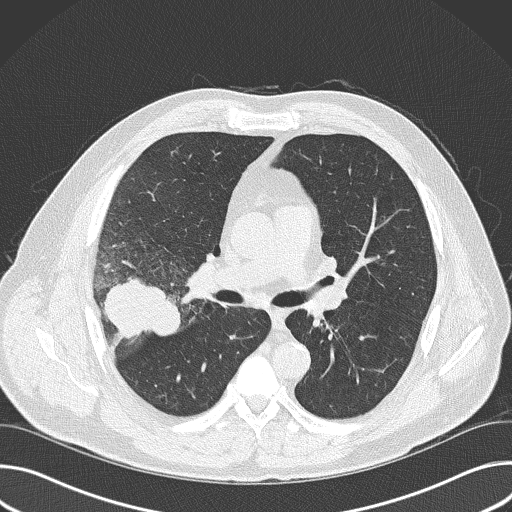
Low-dose screening chest CT, axial slice, first (baseline) screen, lung window (W 1500 / L -600 HU), lung (sharp) reconstruction kernel (B50f), slice 97 of 157 in the series. Male participant, aged 56 years at enrolment.
Lesion marked by an expert reader, box from (x=80, y=258) to (x=184, y=362) px. The exam's reader record, not a measurement of the box and not confirmed to be the same lesion: non-calcified nodule or mass ≥4 mm, right upper lobe, 6 × 5 mm, spiculated (stellate) margins, soft tissue attenuation. Participant outcome: lung cancer diagnosed 16 days after this screen — adenocarcinoma, NOS, right upper lobe, poorly differentiated (G3), stage IIB (AJCC 6th edition), 60 mm at pathology.